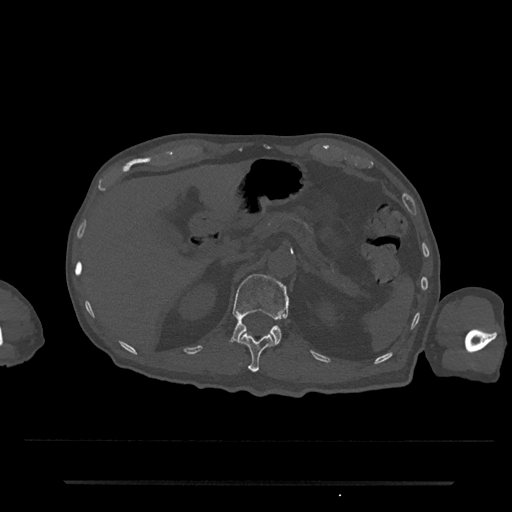
CT including the spine, one axial slice. Slice 163 of 797 in the series (ordered by position). Bone window (W 1800 / L 400 HU). 0.5 mm slice thickness. 512 × 512 image matrix, field of view 427 × 427 mm. Male patient, age 74 years. From the clinical record (not read from this slice): primary cancer: prostate.
Structures marked on this image (semi-automatic segmentation, software-assisted and operator-edited):
- L1 vertebra: box from (x=231, y=274) to (x=289, y=345) px
- T12 vertebra: (x=240, y=333)–(x=273, y=373)